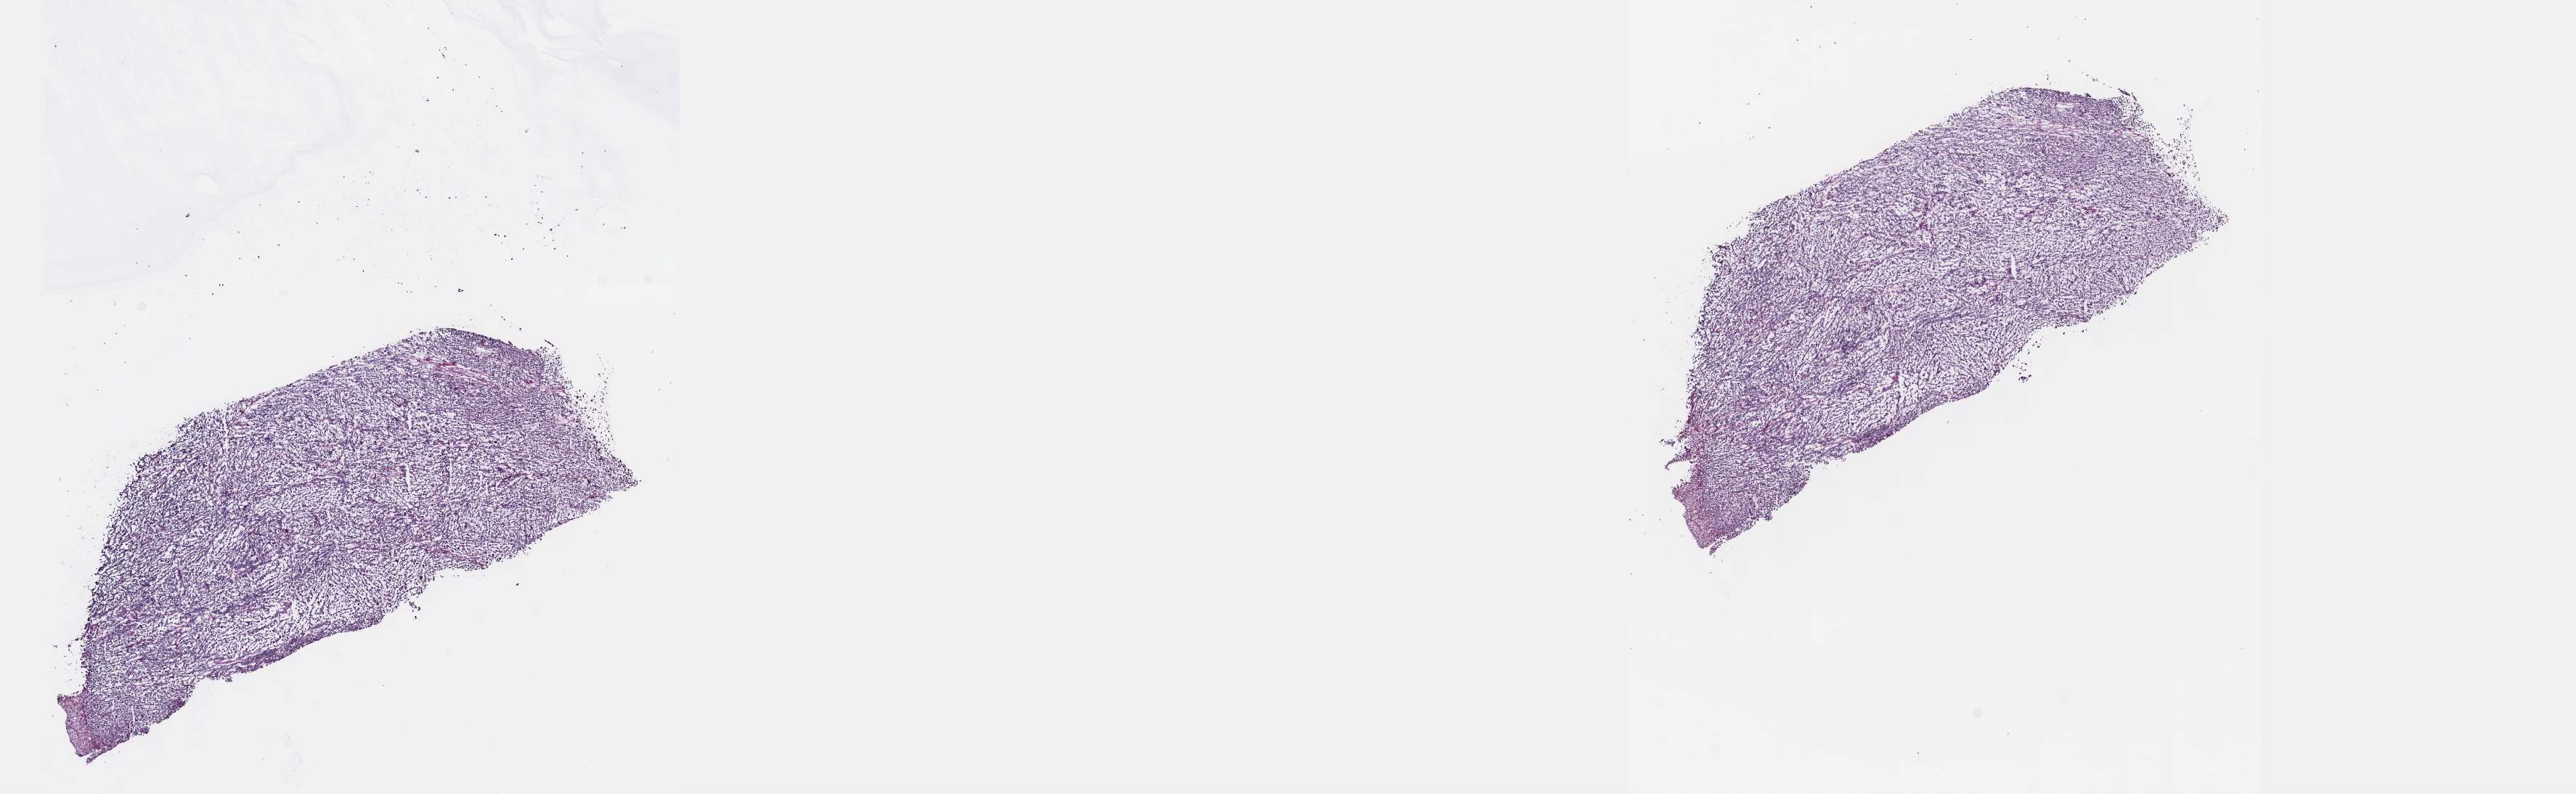
Whole-slide histology image, H&E — shown as a low-resolution overview of the whole scanned area (about 28.7 x 8.8 mm, from a 40x scan), frozen section, metastatic tumour sample, sampled site not recorded. Female patient; age at initial diagnosis 27 years. Pathologist review of this section (percent, as recorded): tumour cells 100%, tumour nuclei 85%, normal cells 0%, stromal cells 0%, necrosis 0%. Infiltration values recorded for this section: lymphocyte infiltration 0%, monocyte infiltration 0%, neutrophil infiltration 0%.
This section: metastatic tumour tissue. Patient diagnosis: Malignant melanoma, NOS.